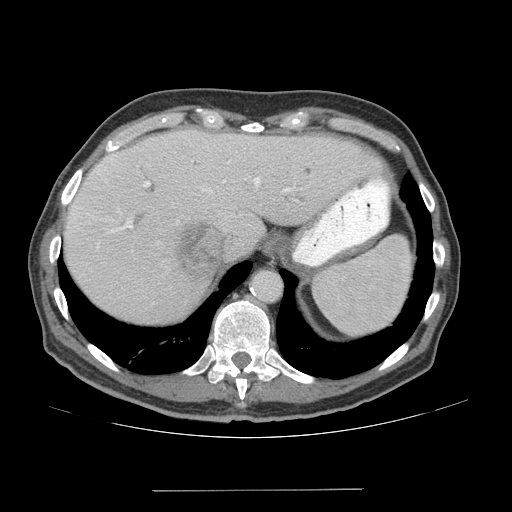
Contrast-enhanced abdominal CT (liver protocol), one axial slice; slice 53 of 77 in the series (ordered by position); reconstruction kernel STANDARD; soft-tissue window (W 400 / L 40 HU); 512 × 512 image matrix, field of view 400 × 400 mm. Case-level facts recorded for this patient, not image findings: diagnosis: hepatocellular carcinoma (patient treated with transarterial chemoembolisation; whether this scan precedes or follows treatment is not stated here); TNM stage (as recorded): Stage-IVA; Child-Pugh class: A; tumour differentiation: well differentiated.
Annotated regions visible in this slice (semi-automatic segmentation, software-assisted and operator-edited):
- liver parenchyma outside the tumour (the mass and vessels are separate outlines, so this box may not span the whole liver): bounding box (x1, y1, x2, y2) in pixels: (64, 128, 380, 324)
- mass: (173, 221, 225, 278)
- liver vessels: (74, 158, 291, 233)